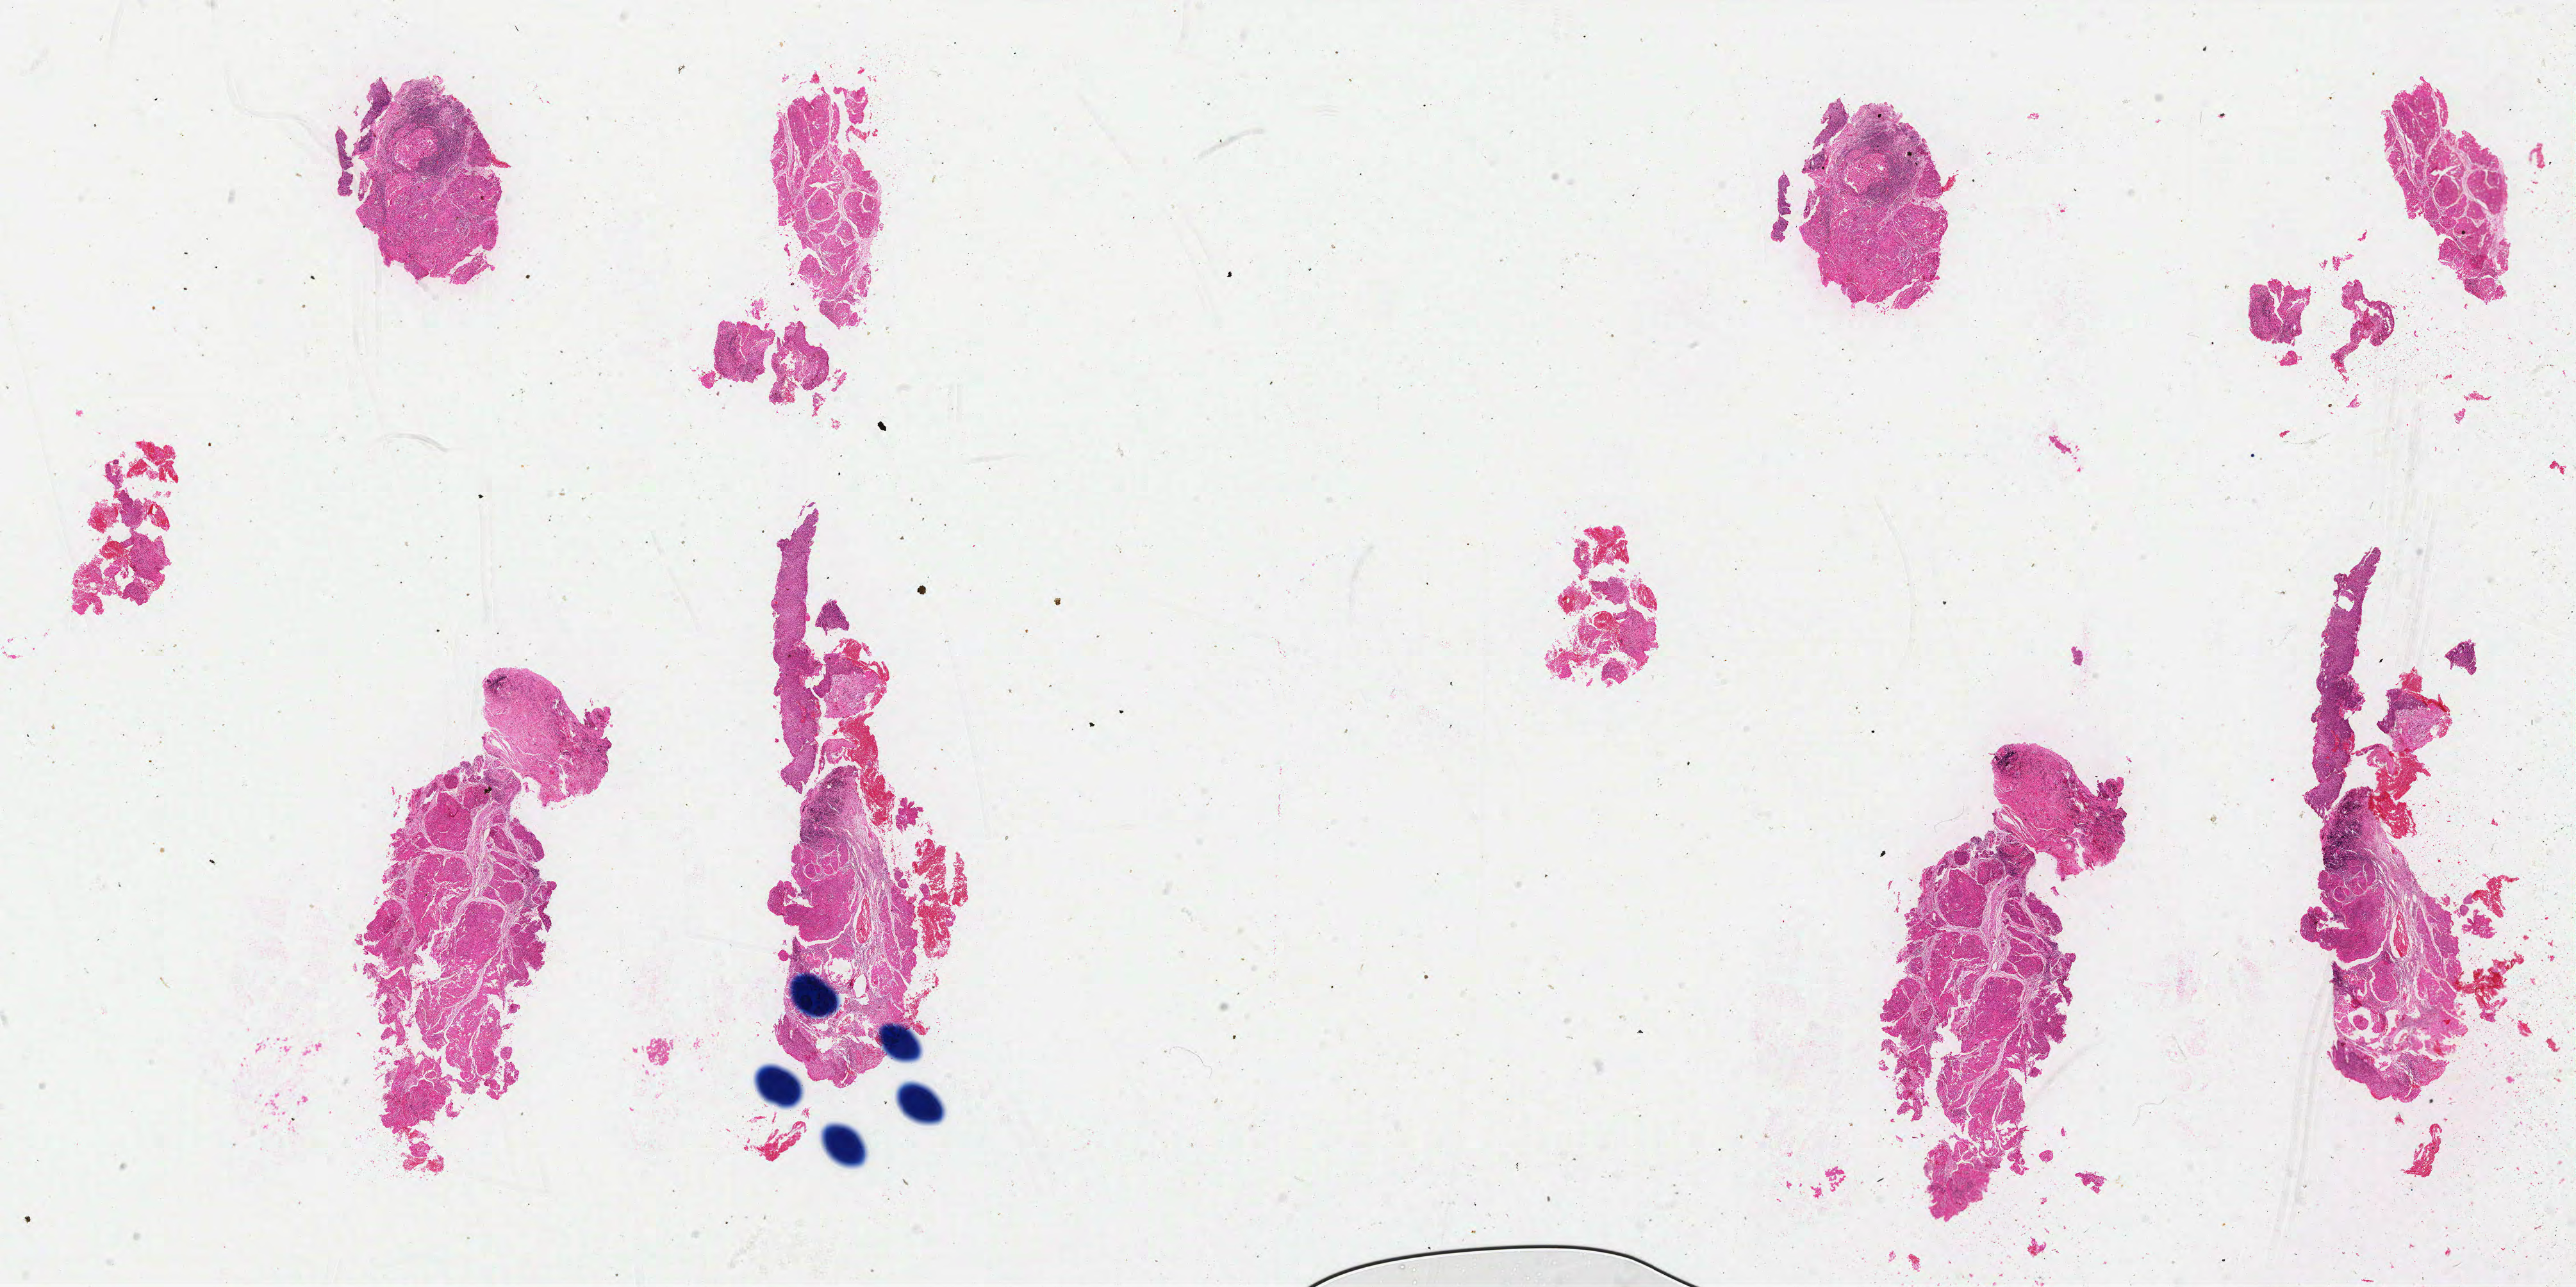
H&E whole-slide image — whole scanned area (about 32.2 x 16.1 mm, from a 40x scan) shown as a low-resolution overview; formalin-fixed paraffin-embedded (FFPE) diagnostic section; primary tumour sample from the cervix. Patient: female, age at initial diagnosis 65 years. Histologic grade: G2 (moderately differentiated).
Histologic diagnosis: Squamous cell carcinoma, NOS (cervix uteri). FIGO stage: IIIB.